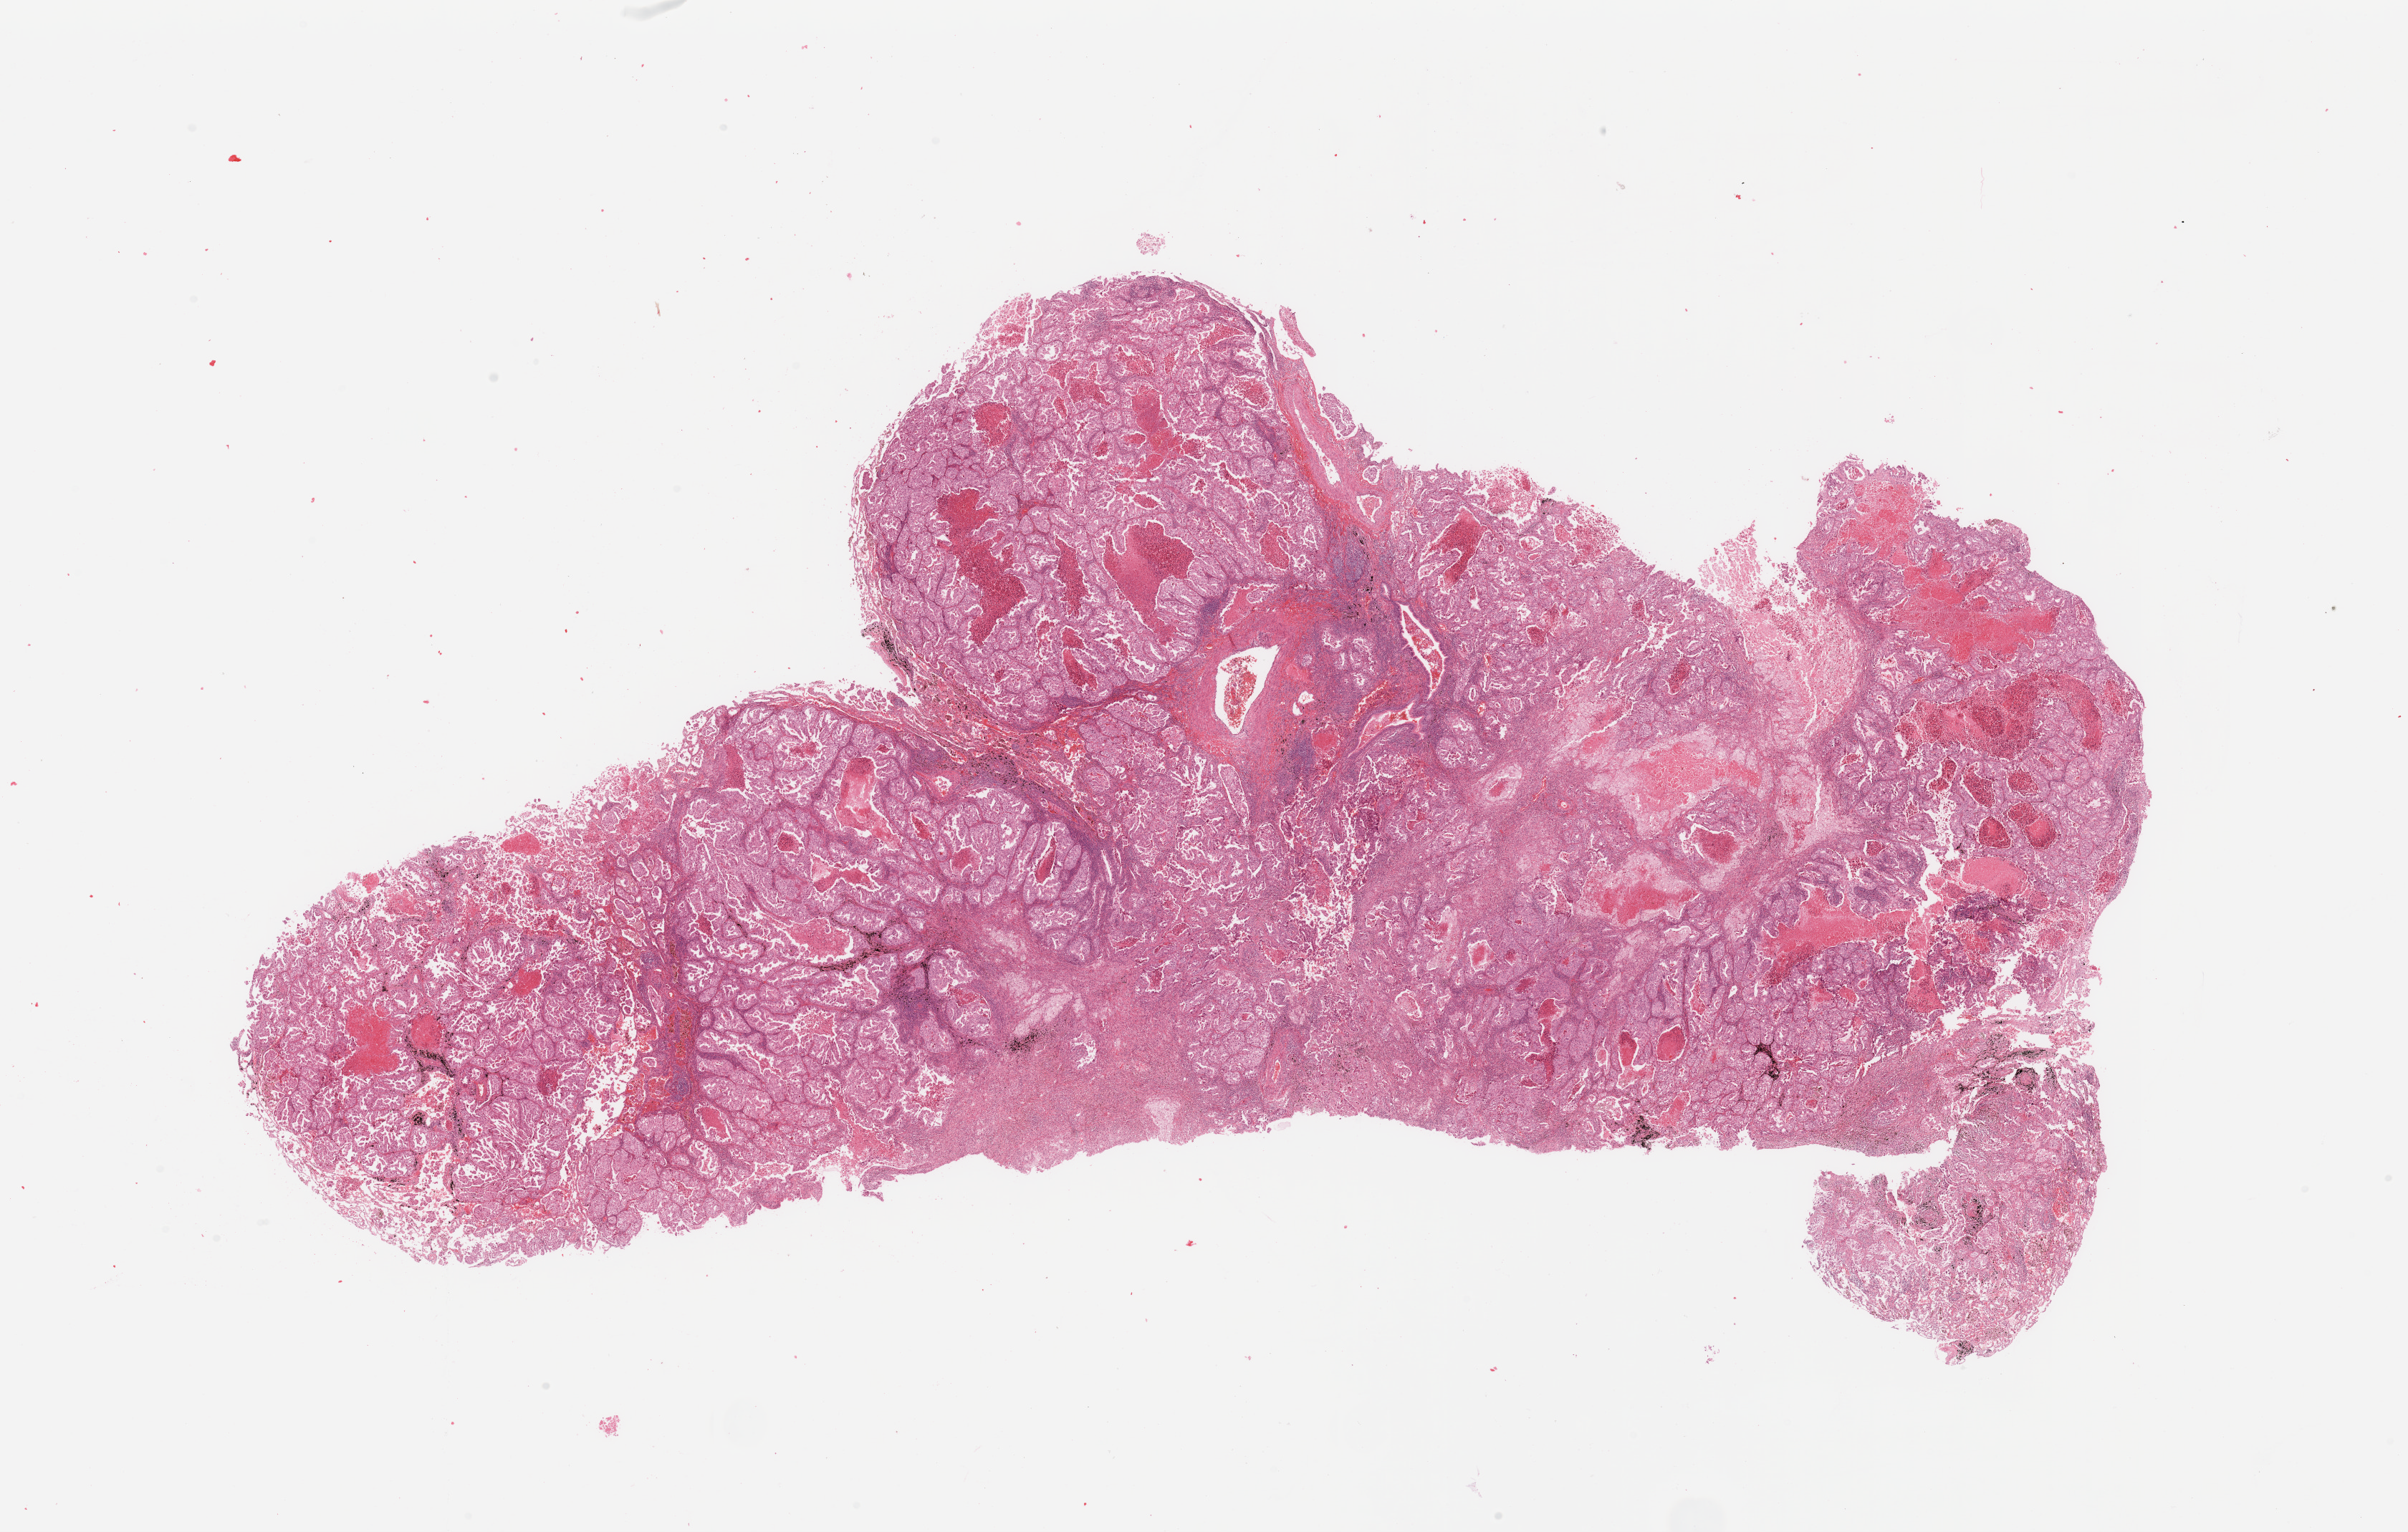
Whole-slide histology image, H&E-stained — shown as a low-resolution overview of the whole scanned area (about 26.6 x 16.9 mm, from a 20x scan). Lung, tumour tissue. Patient: male, age 48 years. Histologic grade: G2 (moderately differentiated).
• primary tumour site (as recorded): right lower lobe
• diagnosis: Adenocarcinoma, NOS
• AJCC pathologic stage: IB